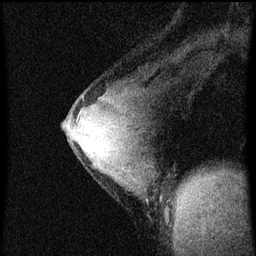
Breast MRI (dynamic contrast-enhanced), one sagittal slice. Slice 37 of 60 in the series (ordered by position). Dynamic contrast-enhanced series, image 2 of 4 at this slice position (ordered by acquisition). 1.5 T. TE 4.2 ms, TR 8 ms. 2 mm slice thickness. 256 × 256 image matrix, field of view 180 × 180 mm. Female patient, age 33 years.
Outlined on this slice (semi-automatic segmentation, software-assisted and operator-edited):
- analysis volume of interest (the breast-tissue region the enhancement analysis was run in; not a lesion): bounding box [x1, y1, x2, y2] px = [64, 78, 166, 217]
- tumour enhancement mask (voxels above the 70 % enhancement threshold inside the analysis volume of interest): [76, 112, 84, 151]